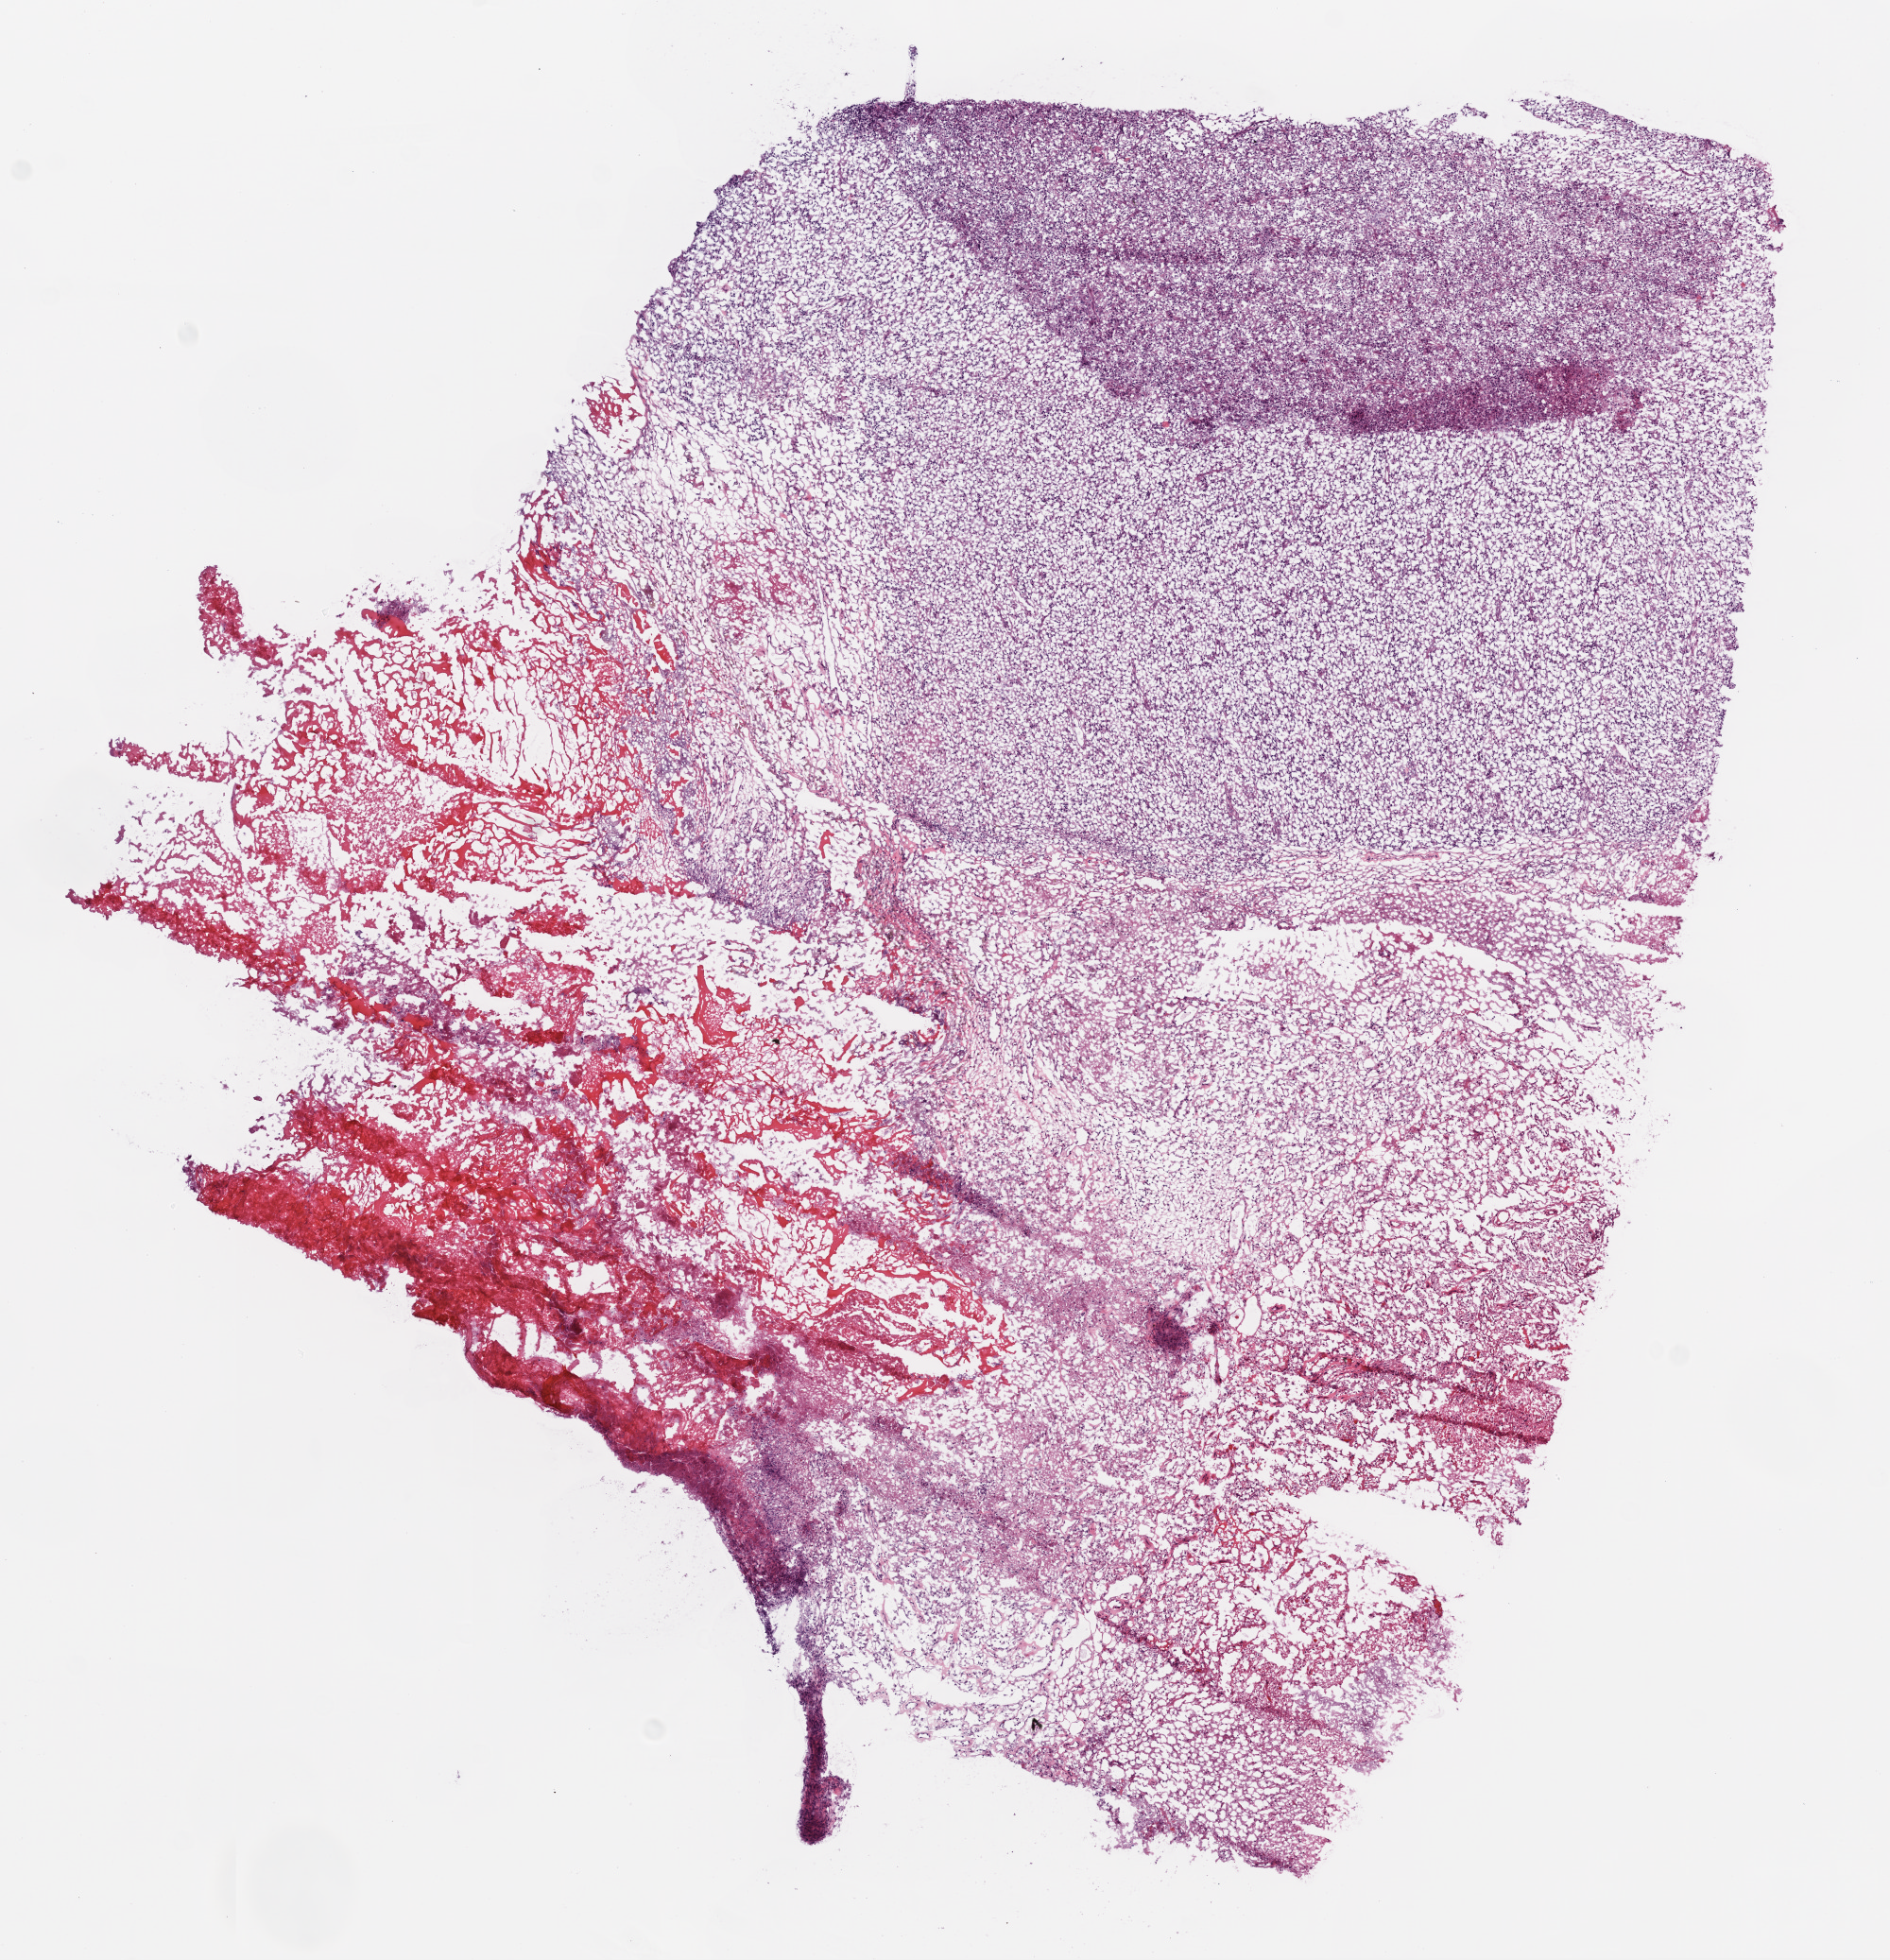
Digitized H&E tissue section (whole slide) — shown as a low-resolution overview of the whole scanned area (about 8.0 x 8.3 mm, acquisition: 20x scan), frozen section from the top of the tissue portion, sample: primary tumour, brain. Patient: male, age at initial diagnosis 53 years. Pathologist review of this section (percent, as recorded): tumour cells 60%, tumour nuclei 90%, normal cells 0%, stromal cells 10%, necrosis 30%.
* histologic diagnosis: Glioblastoma